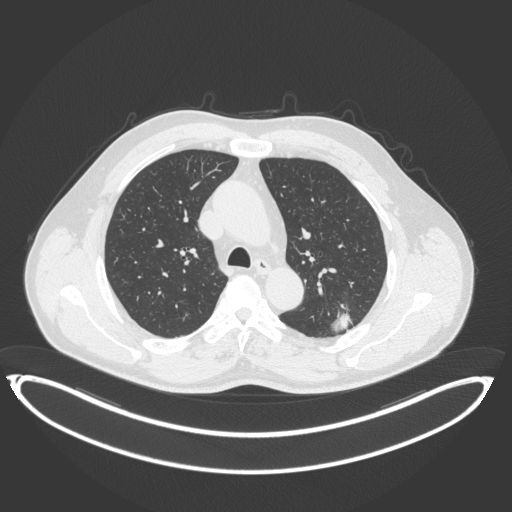
Chest CT, one axial slice; position 250 of 399 along the scan axis; 120 kVp; lung window (W 1500 / L -600 HU); 512 × 512 image matrix, field of view 469 × 469 mm. Male patient, age 58 years. From the clinical record (not read from this slice): clinical TNM (as recorded): T1c N0 M0.
Outlined on this slice (bounding box drawn by a radiologist):
- lung tumour (recorded histology: adenocarcinoma): bounding box <326,301,358,337> (left, top, right, bottom; pixels)